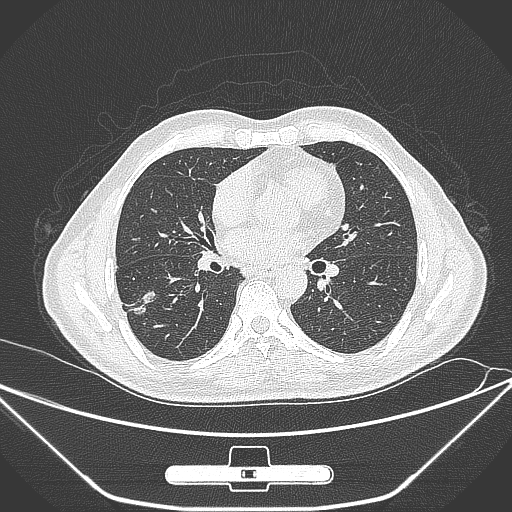
Chest CT, one axial slice; position 140 of 309 along the scan axis; 120 kVp; lung window (W 1500 / L -600 HU); 1 mm slice thickness; 512 × 512 image matrix, field of view 398 × 398 mm. Male patient, age 71 years. From the clinical record (not read from this slice): clinical TNM (as recorded): T1c N0 M0.
Structures marked on this image (rectangle marked by the reading radiologist):
- lung tumour (recorded histology: adenocarcinoma): bounding box <131,288,158,313> (left, top, right, bottom; pixels)